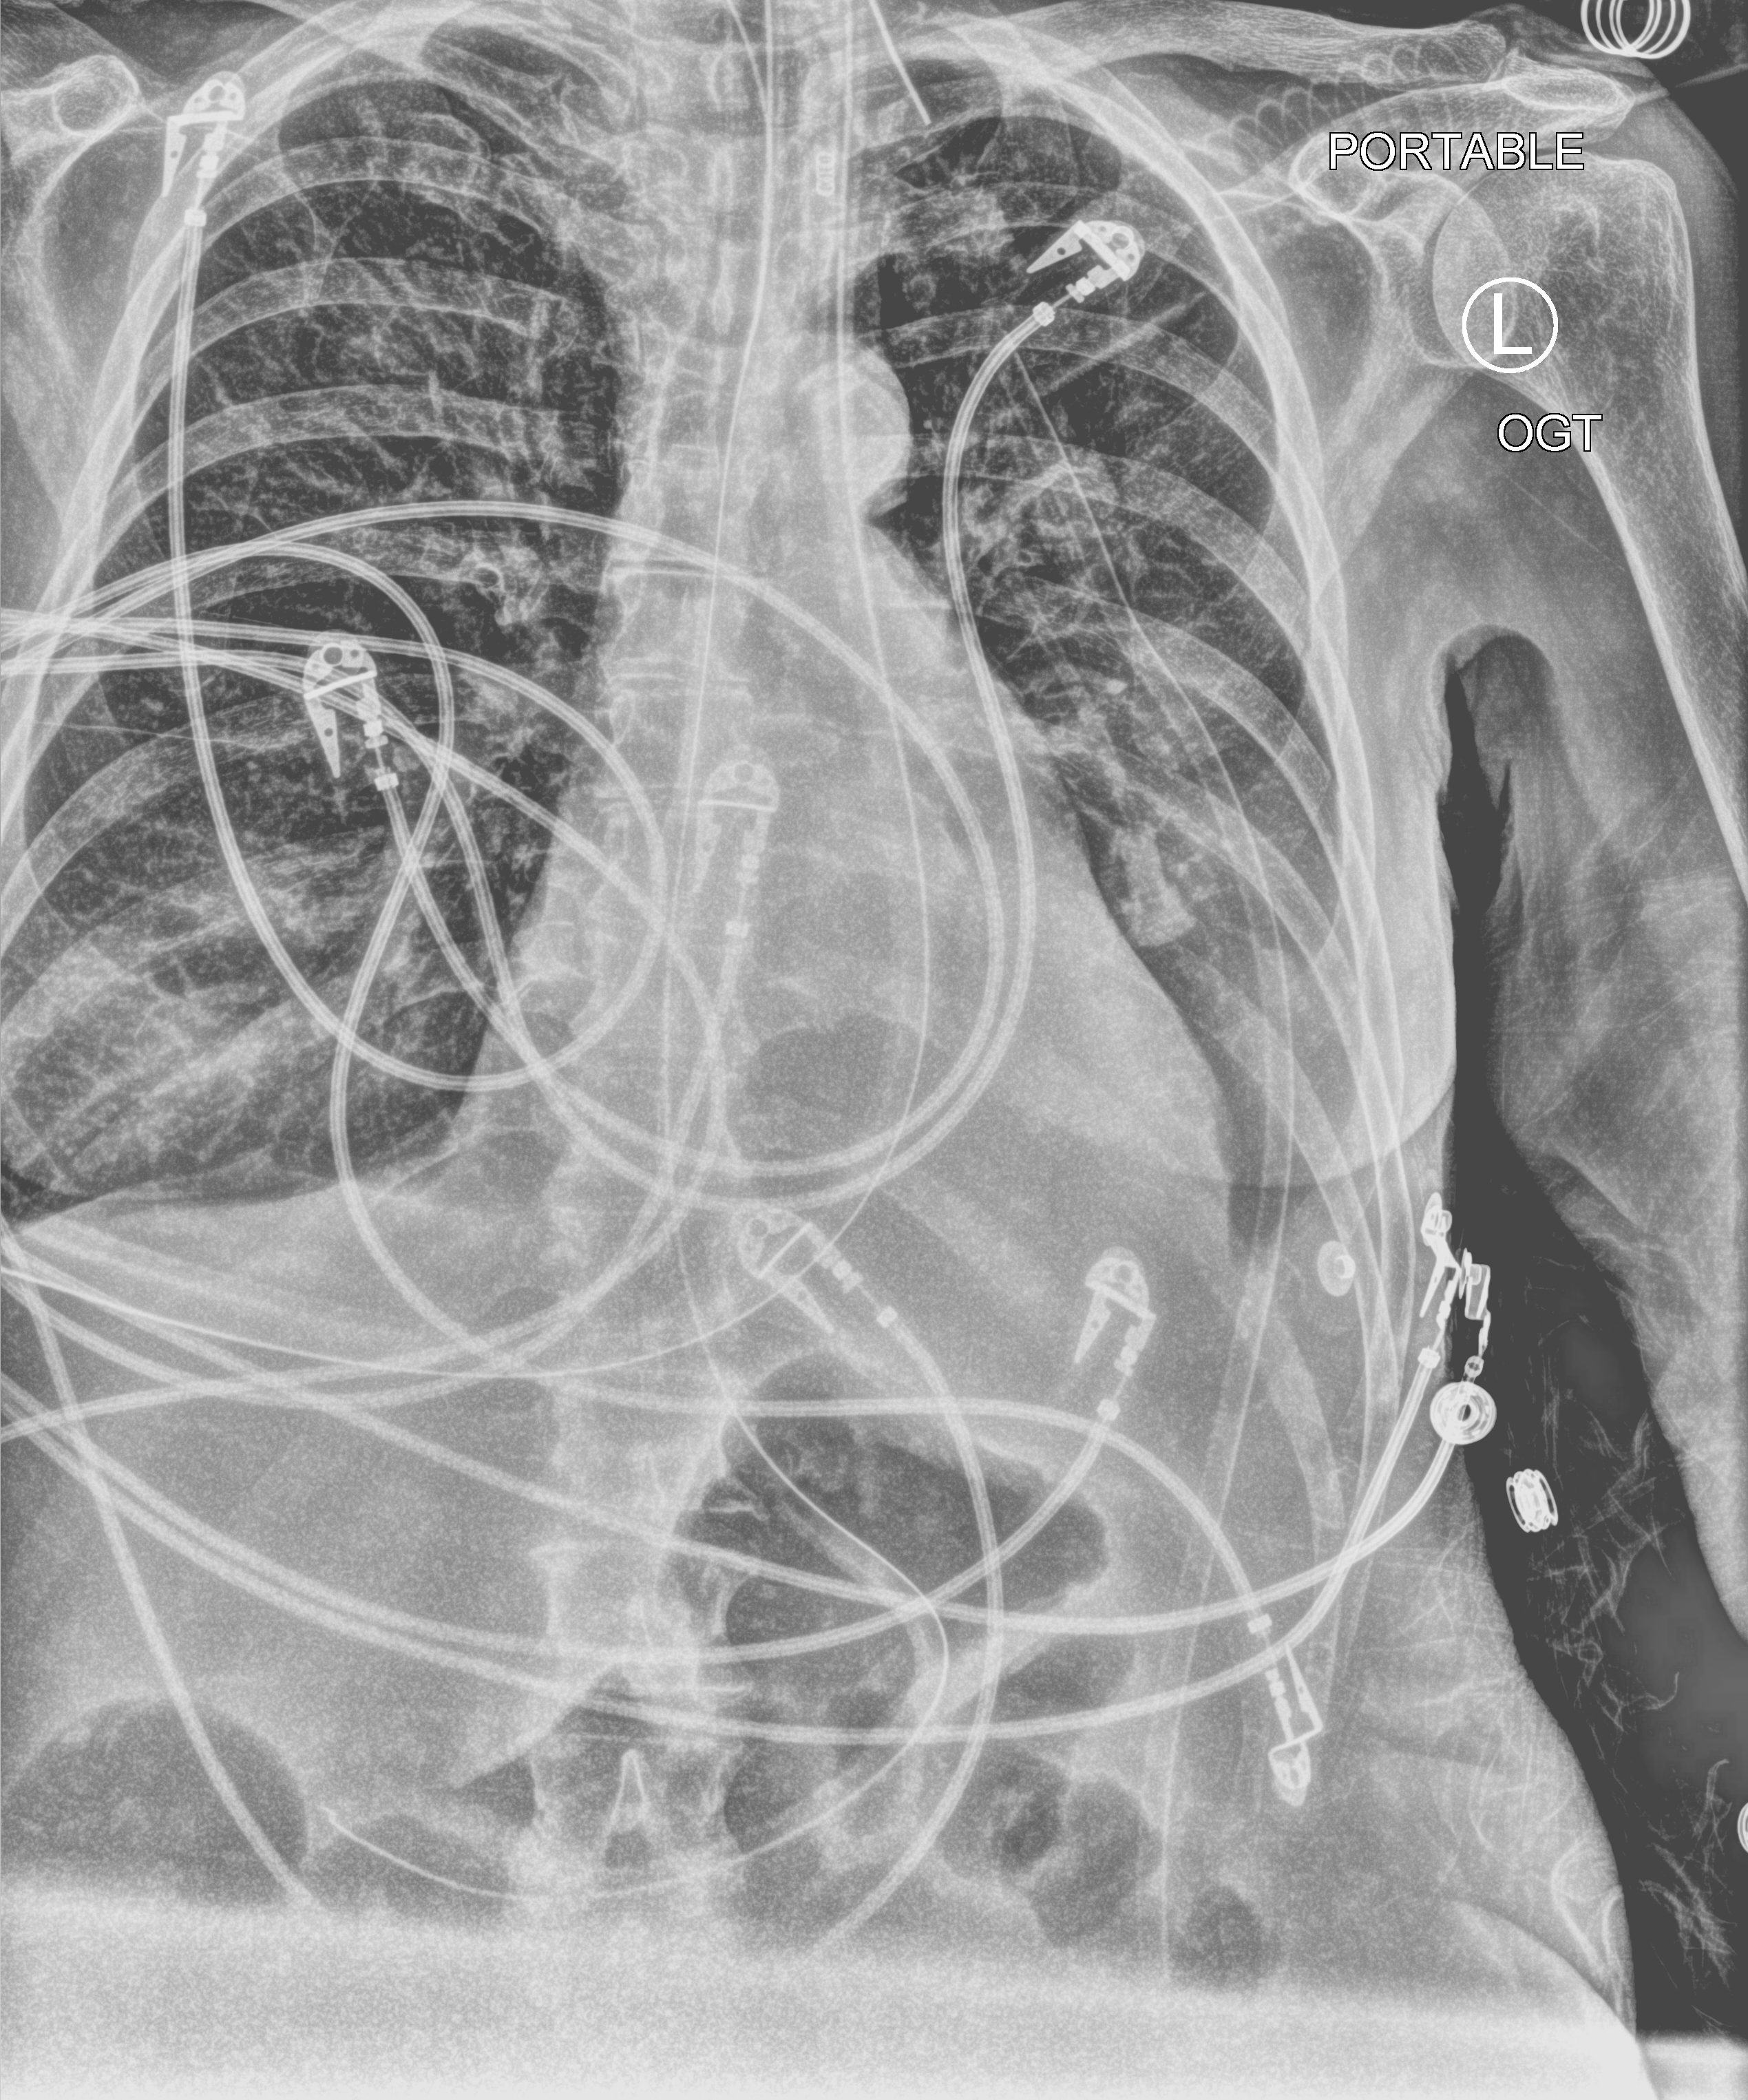
Bedside chest radiograph (computed radiography); anteroposterior (AP) projection. Female patient hospitalised with COVID-19, age 60–74 years.
From the hospital-stay record, not from the radiograph (when in the stay this image was taken is not recorded):
- mechanically ventilated during this hospital stay: yes
- admitted to intensive care during this hospital stay: yes